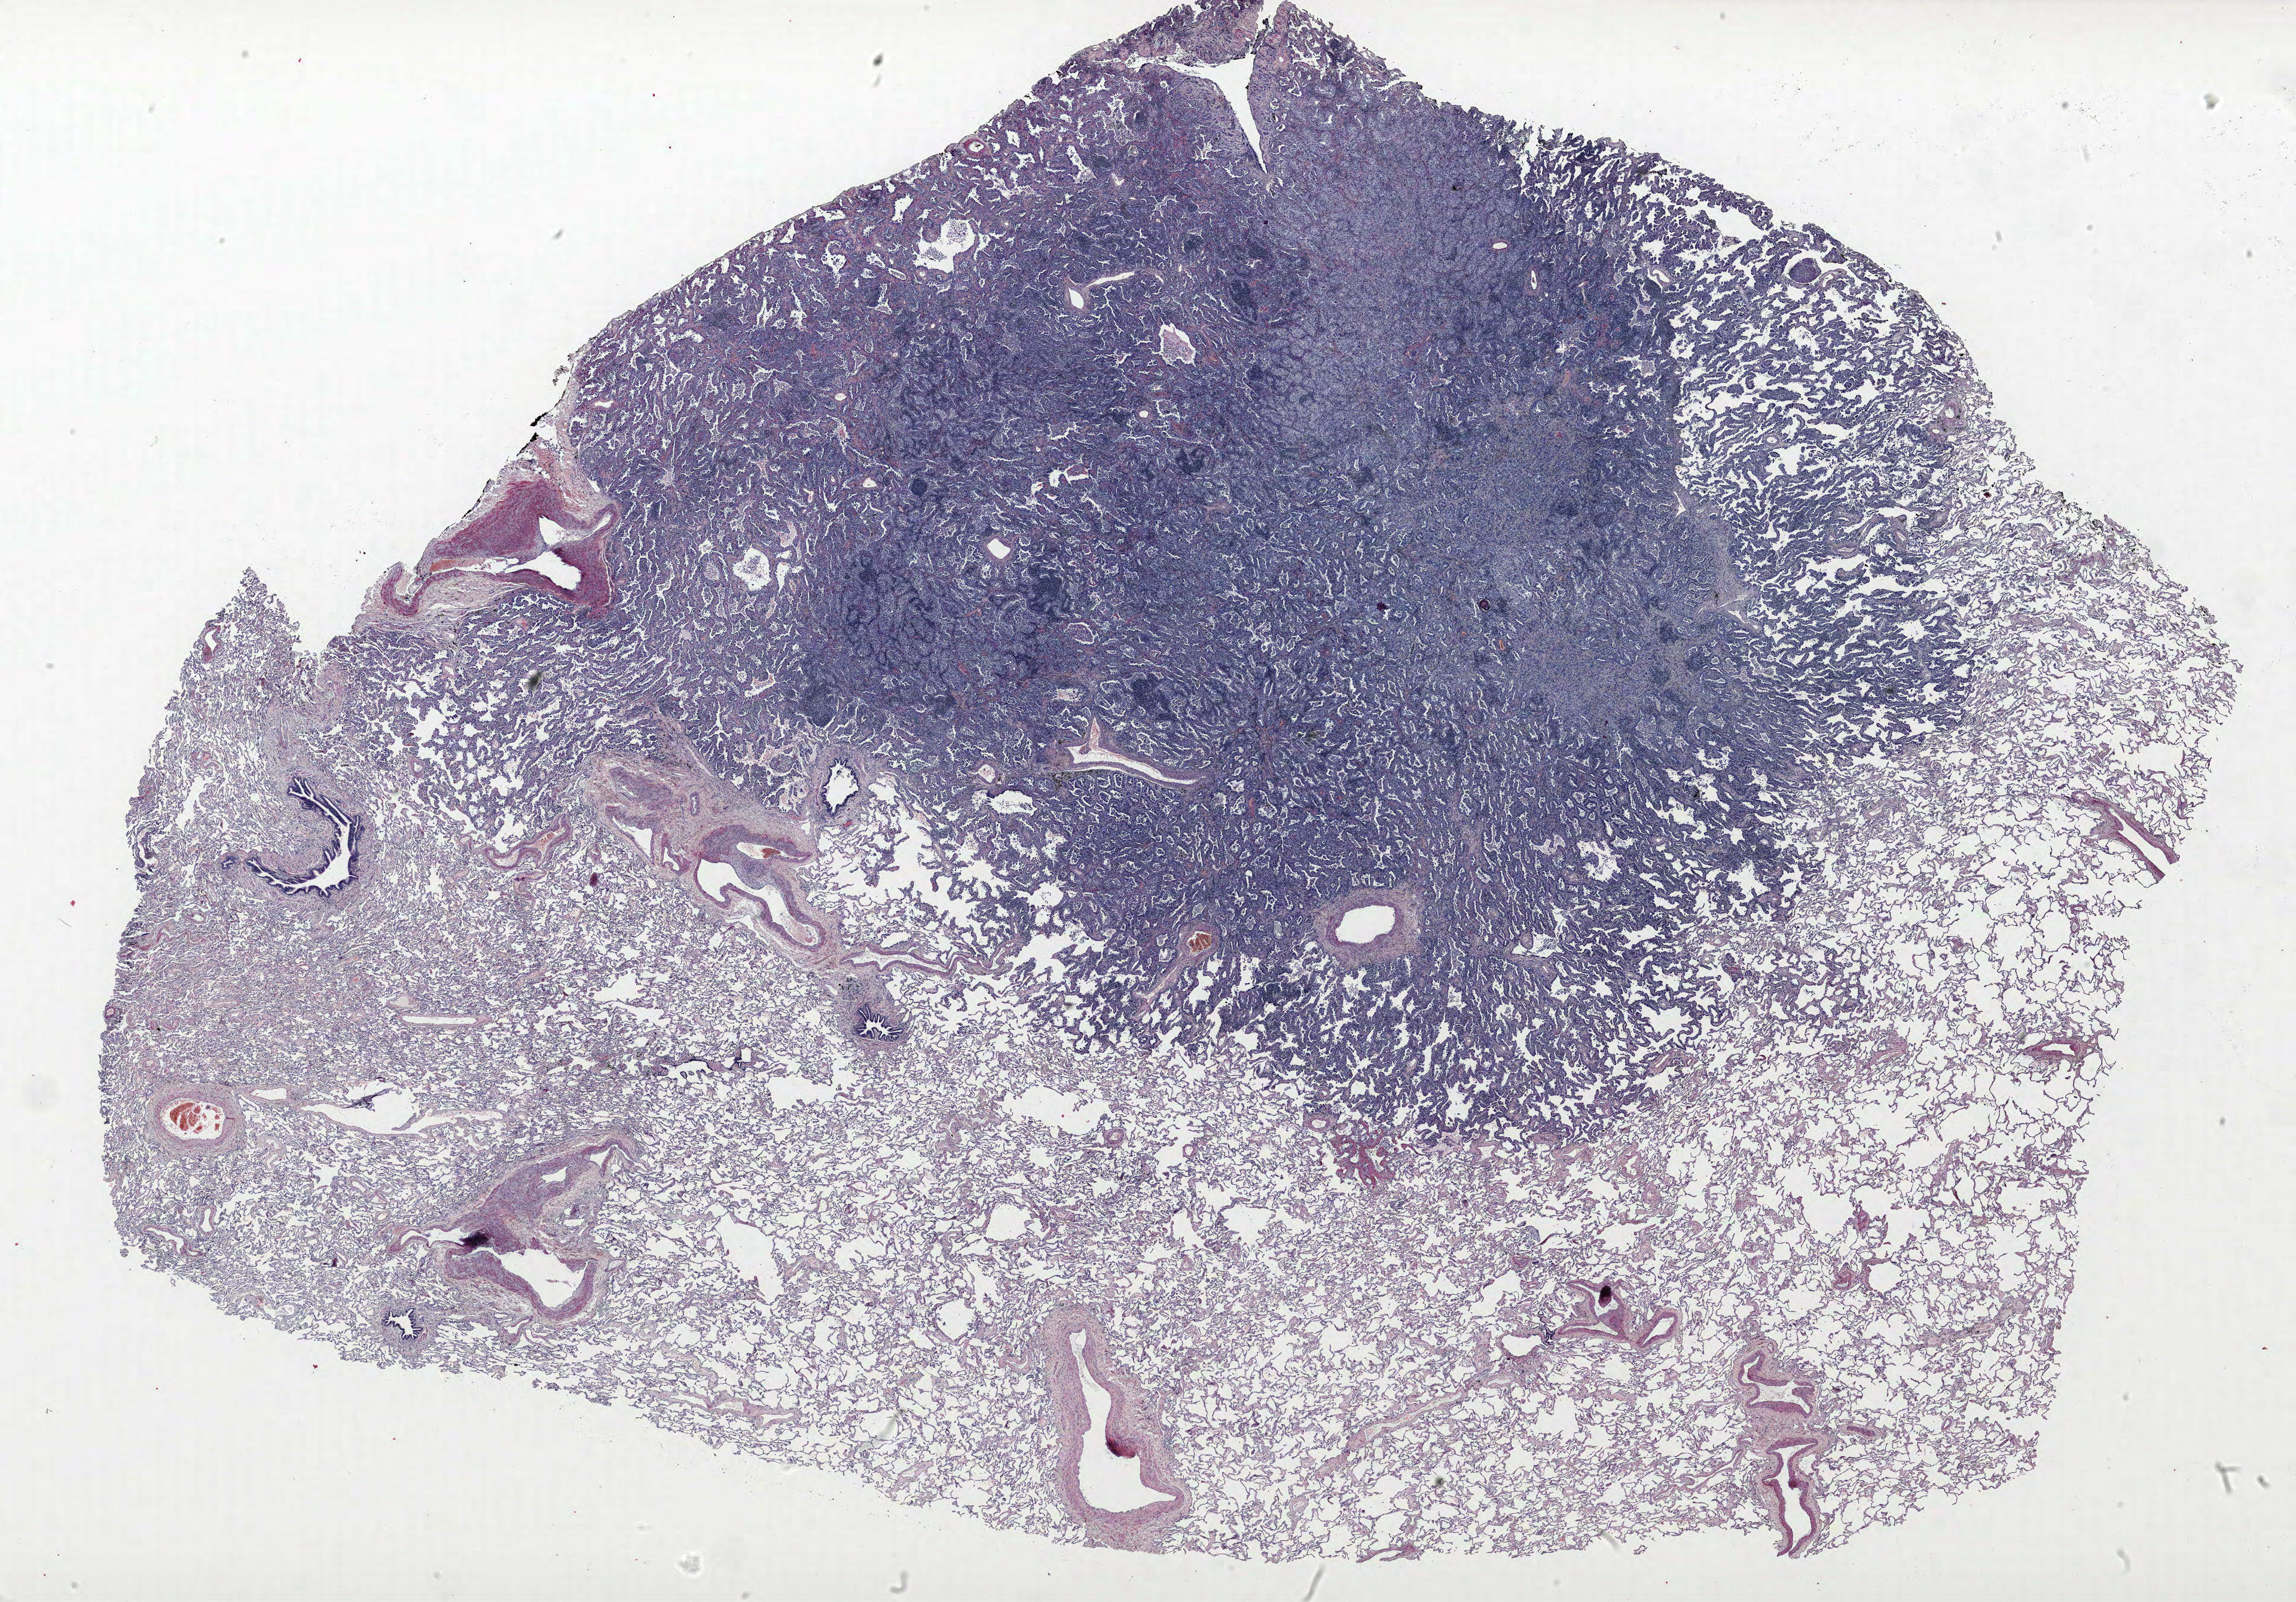
Whole-slide histology image, Hematoxylin and eosin (H&E) stained — whole scanned area (about 30.7 x 21.4 mm) shown as a low-resolution overview; formalin-fixed paraffin-embedded (FFPE) section; lung tissue. Male patient, aged 71 at enrolment. Former smoker at enrolment. Grade: moderately differentiated (G2).
Primary tumour location (clinical record): right upper lobe. Tumour size (pathology): 25 mm. Participant's lung-cancer diagnosis: Bronchiolo-alveolar adenocarcinoma, NOS. Stage (AJCC 6th edition): IIIA.